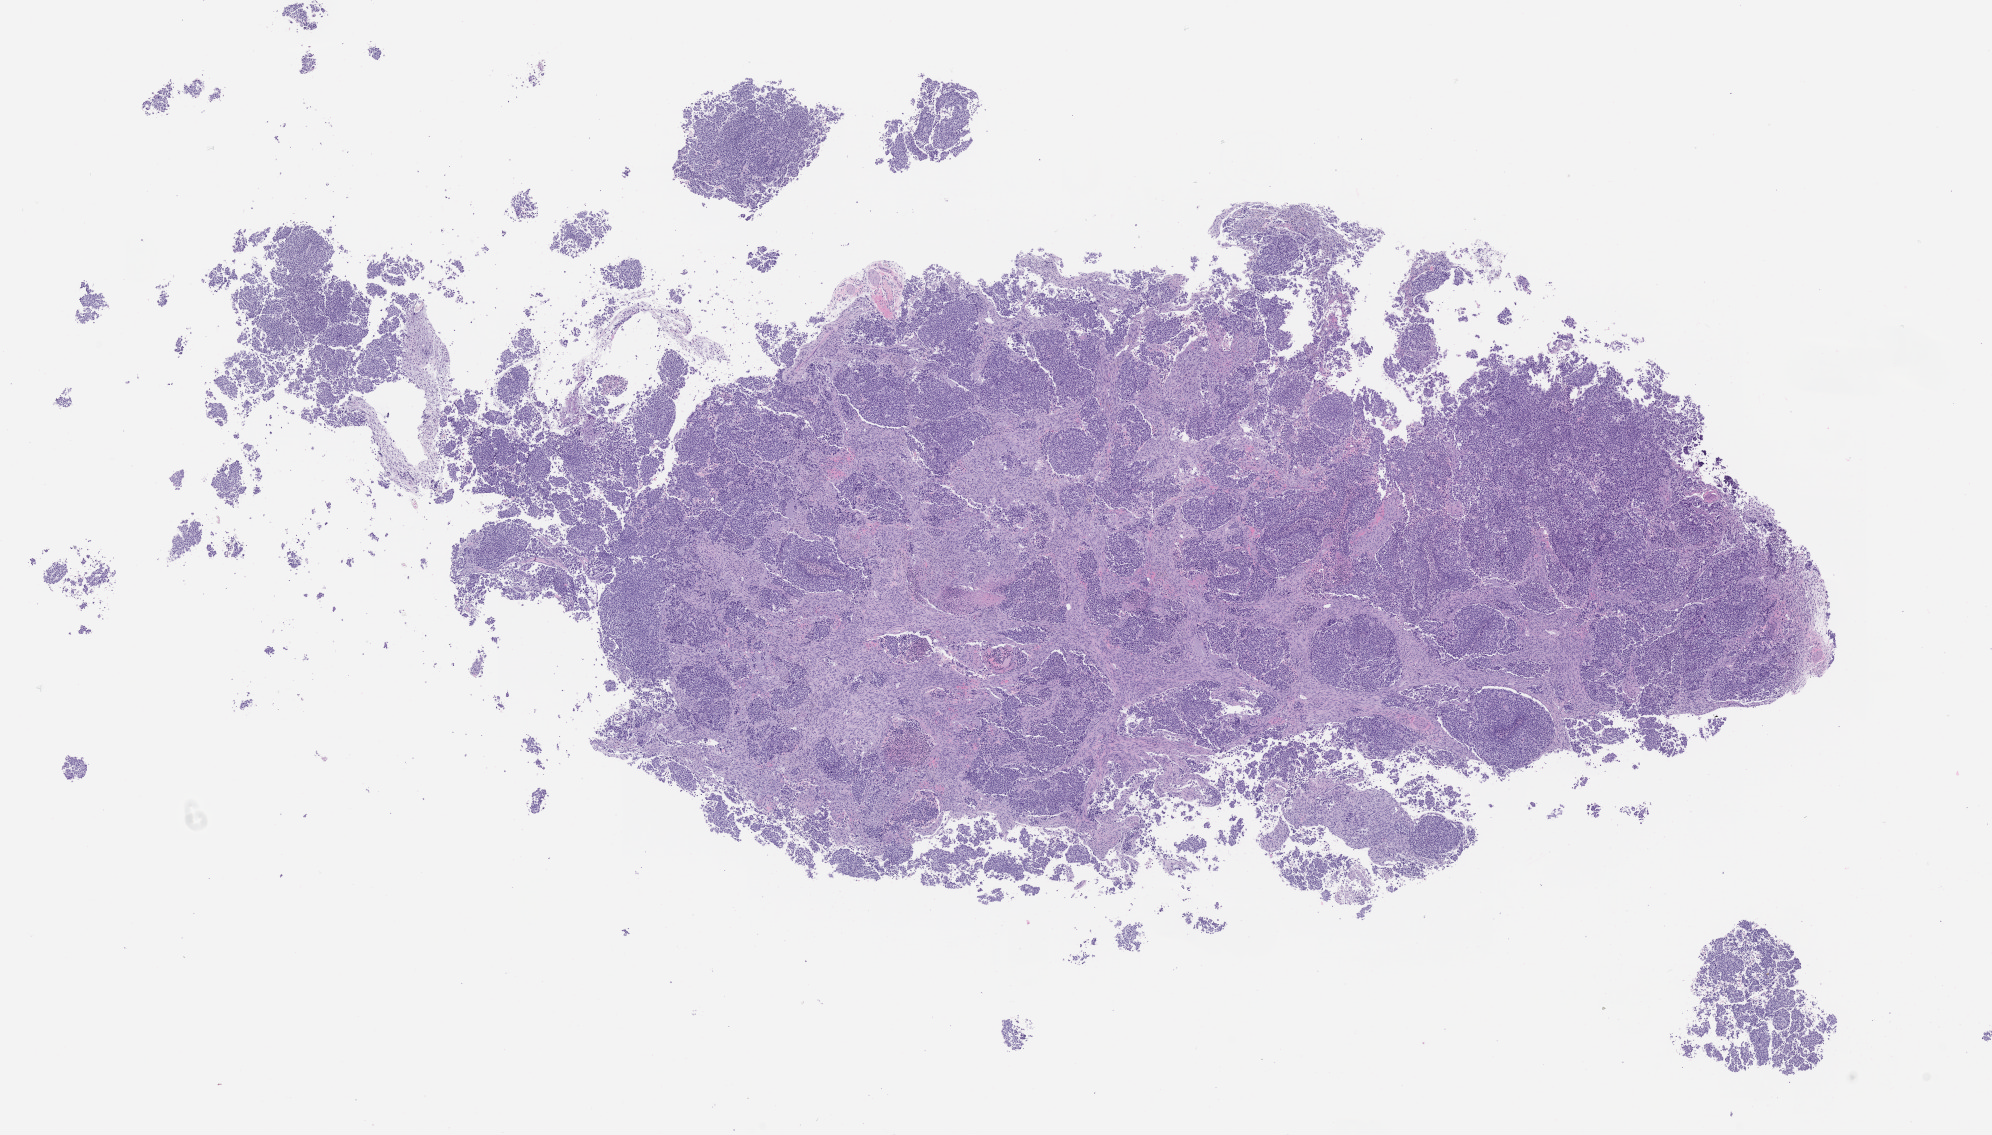
Whole-slide image, hematoxylin and eosin (H&E): patient-derived xenograft (human tumor grown in a mouse), a low-resolution overview of the entire scanned area, about 16.0 x 9.1 mm, formalin-fixed paraffin-embedded section, tumor site category: lung.
- originating patient diagnosis: Lung Adenocarcinoma